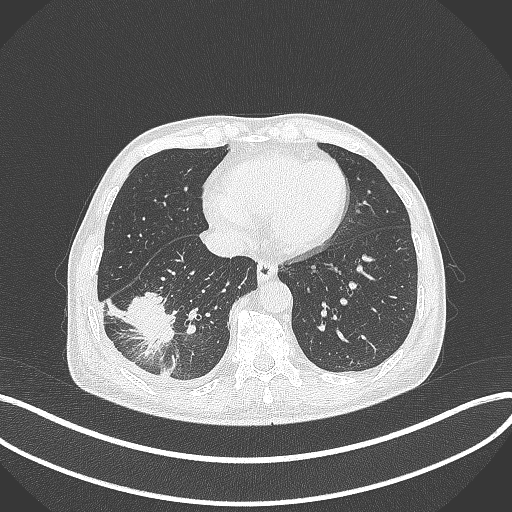
Chest CT, one axial slice. Slice 115 of 388 in the series (ordered by position). 120 kVp. Lung window (W 1500 / L -600 HU). 512 × 512 image matrix, field of view 400 × 400 mm. Male patient, age 64 years. Case-level facts recorded for this patient, not image findings: clinical TNM (as recorded): T3 N0 M0.
Structures marked on this image (bounding box drawn by a radiologist):
- lung tumour (recorded histology: adenocarcinoma): box from (x=117, y=289) to (x=177, y=362) px